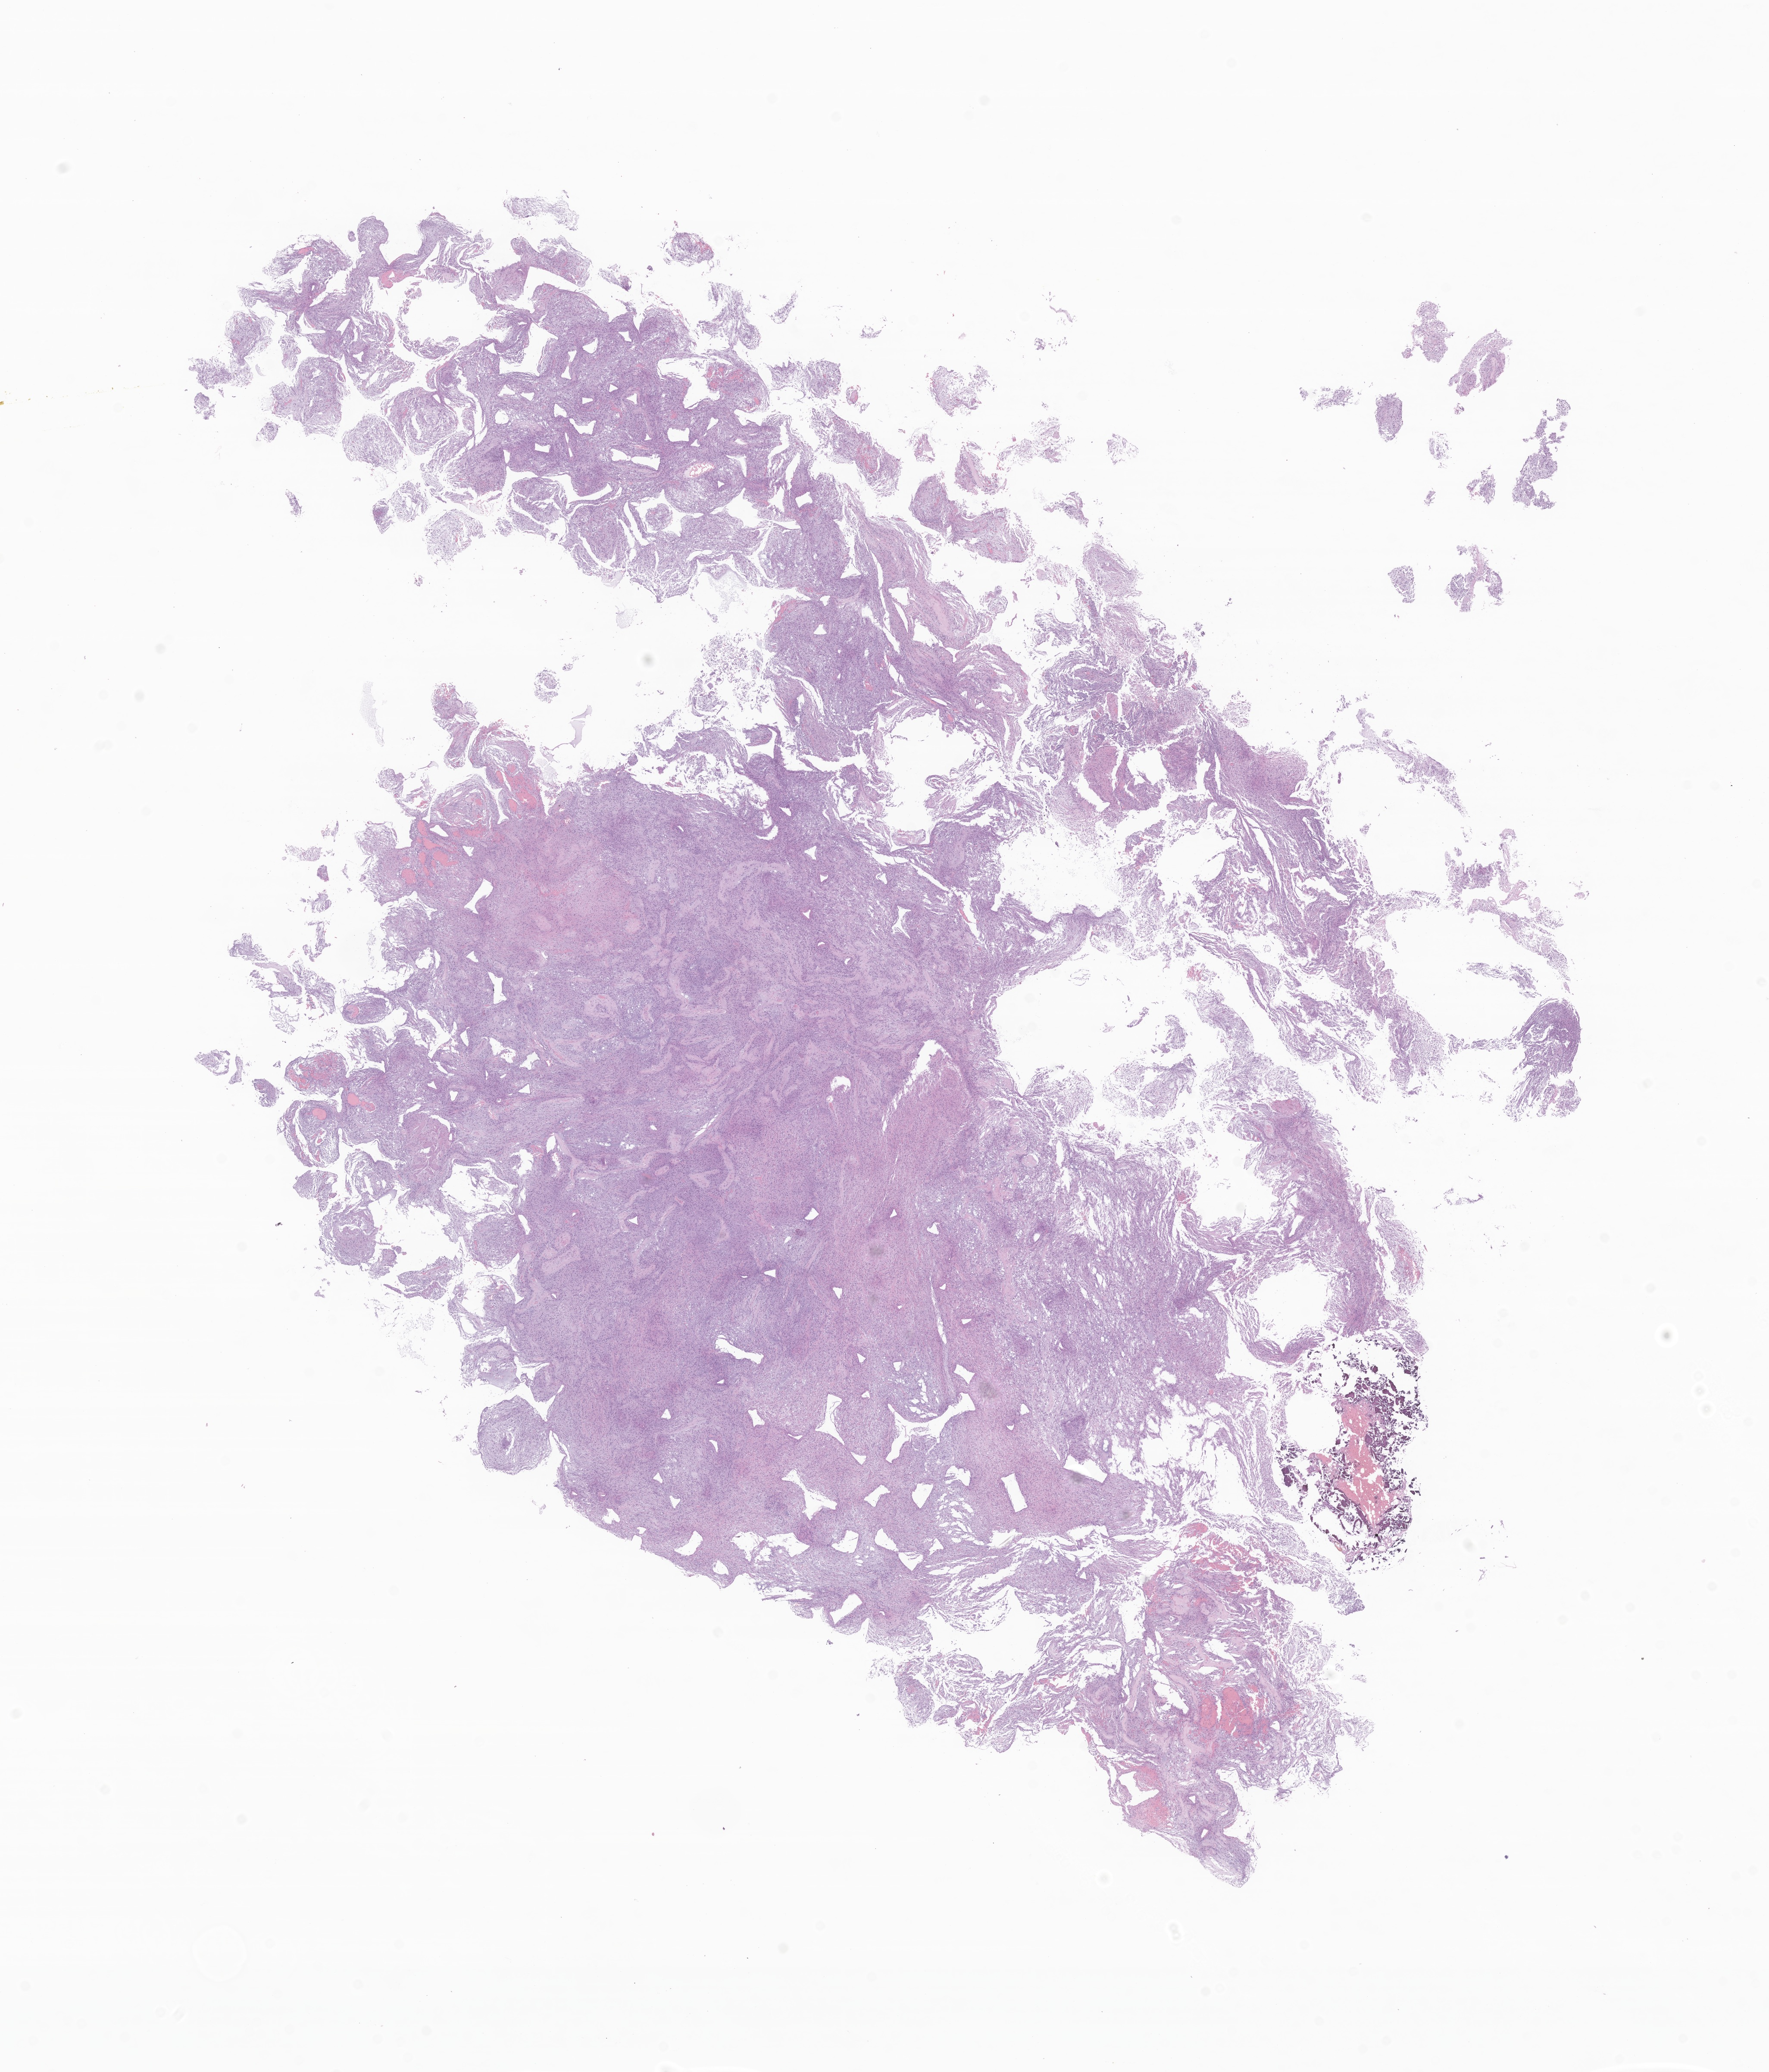
Haematoxylin and eosin whole-slide image of tumor tissue from the brain, whole scanned area (about 17.3 x 20.3 mm) shown as a low-resolution overview. Formalin-fixed, paraffin-embedded (FFPE) tissue. Patient male; age 203 months (16 years 11 months).
• recorded diagnosis: Neoplasm, uncertain whether benign or malignant